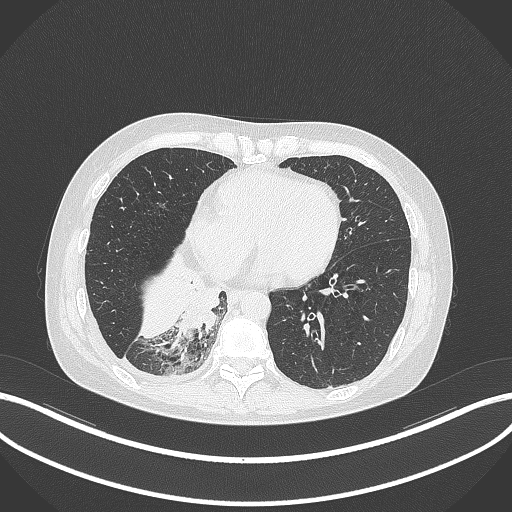
Chest CT, one axial slice; slice 102 of 329 in the series (ordered by position); lung window (W 1500 / L -600 HU); 512 × 512 image matrix. Patient: female, 63 years. Case-level facts recorded for this patient, not image findings: clinical TNM (as recorded): T1c N0 M0.
Outlined on this slice (bounding box drawn by a radiologist):
- lung tumour (recorded histology: adenocarcinoma): box from (x=181, y=282) to (x=224, y=335) px